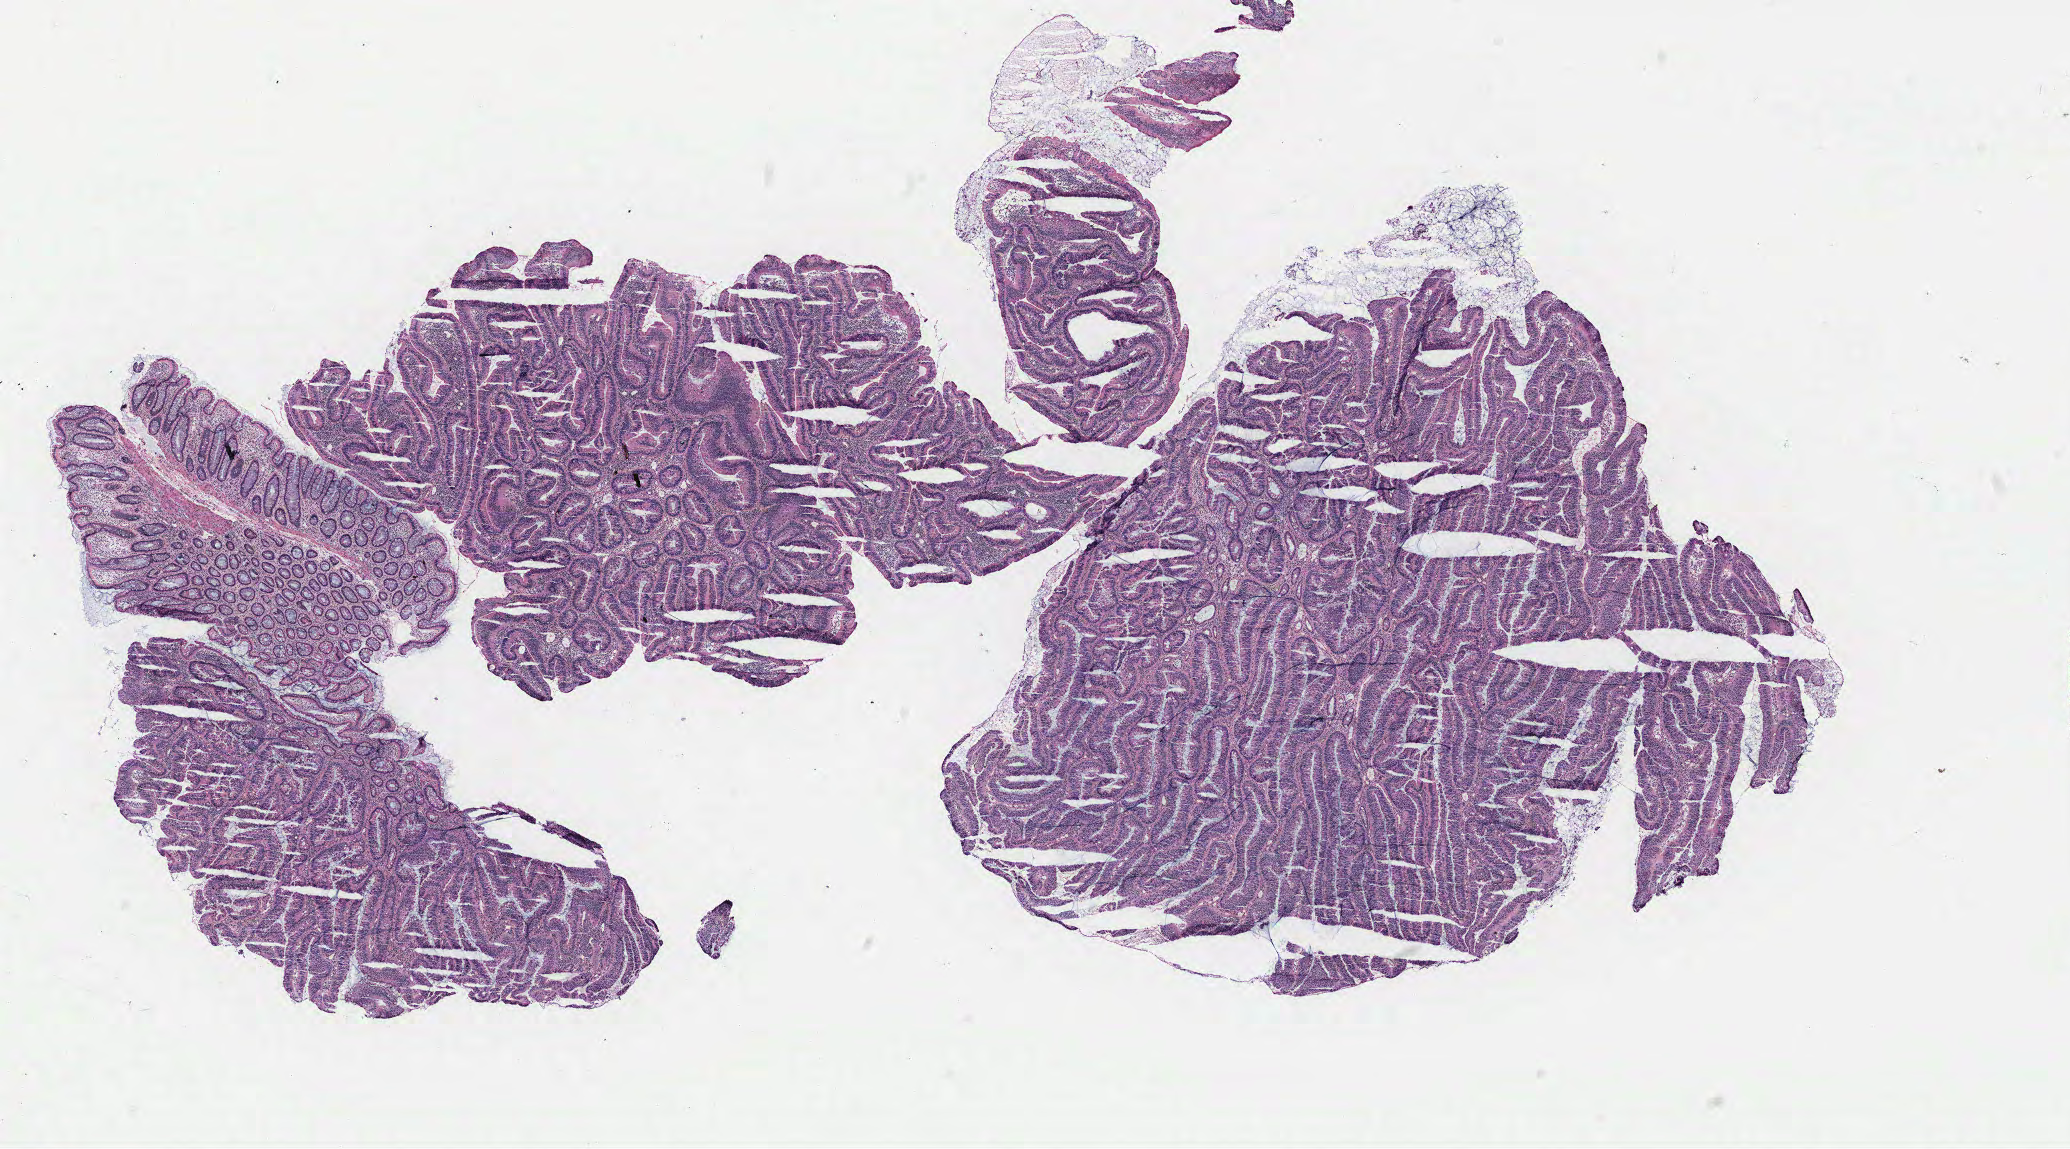
Digitized Hematoxylin and eosin (H&E) stained tissue section (whole slide) — shown as a low-resolution overview of the whole scanned area (about 16.6 x 9.2 mm, from a 40x scan); normal (non-tumour) tissue sample, colon. 54-year-old female patient.
- this section: normal (non-tumour) tissue from the same patient
- patient diagnosis: Adenocarcinoma, NOS